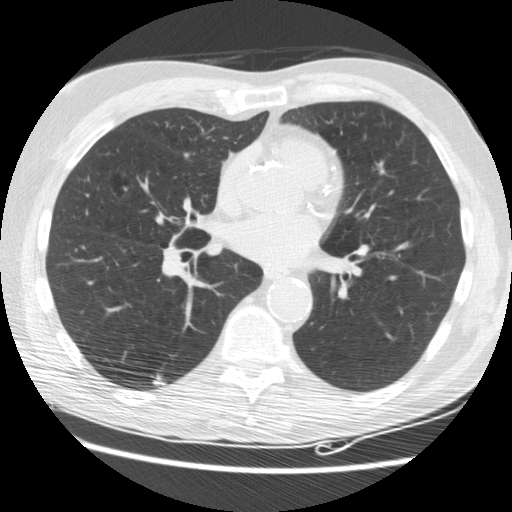
Low-dose screening chest CT, one axial slice; position 83 of 176 along the scan axis; reconstruction kernel STANDARD; lung window (W 1500 / L -600 HU); 512 × 512 image matrix, field of view 347 × 347 mm.
Outlined on this slice (manually delineated by an expert):
- lesion 2 (tumor, lower lobe of right lung): bounding box [x1, y1, x2, y2] px = [151, 373, 167, 387]